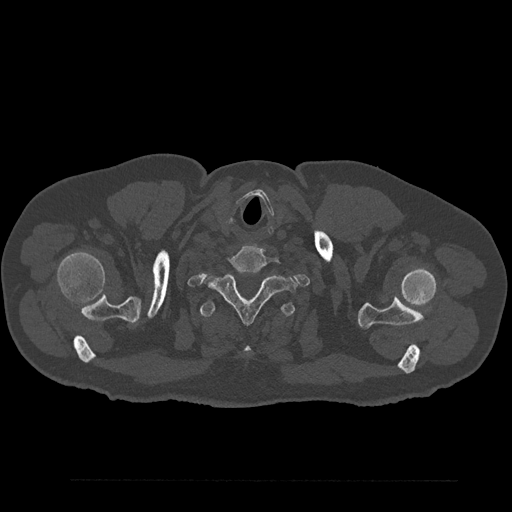
CT including the spine, one axial slice. Position 752 of 797 along the scan axis. Reconstruction kernel Br40s/3. 120 kVp. Bone window (W 1800 / L 400 HU). 0.5 mm slice thickness. 512 × 512 image matrix, field of view 430 × 430 mm. Patient: male, 61 years. From the clinical record (not read from this slice): primary cancer: prostate.
Structures marked on this image (semi-automatic segmentation, software-assisted and operator-edited):
- T1 vertebra: box from (x=204, y=271) to (x=297, y=323) px
- T2 vertebra: (x=200, y=300)–(x=296, y=354)